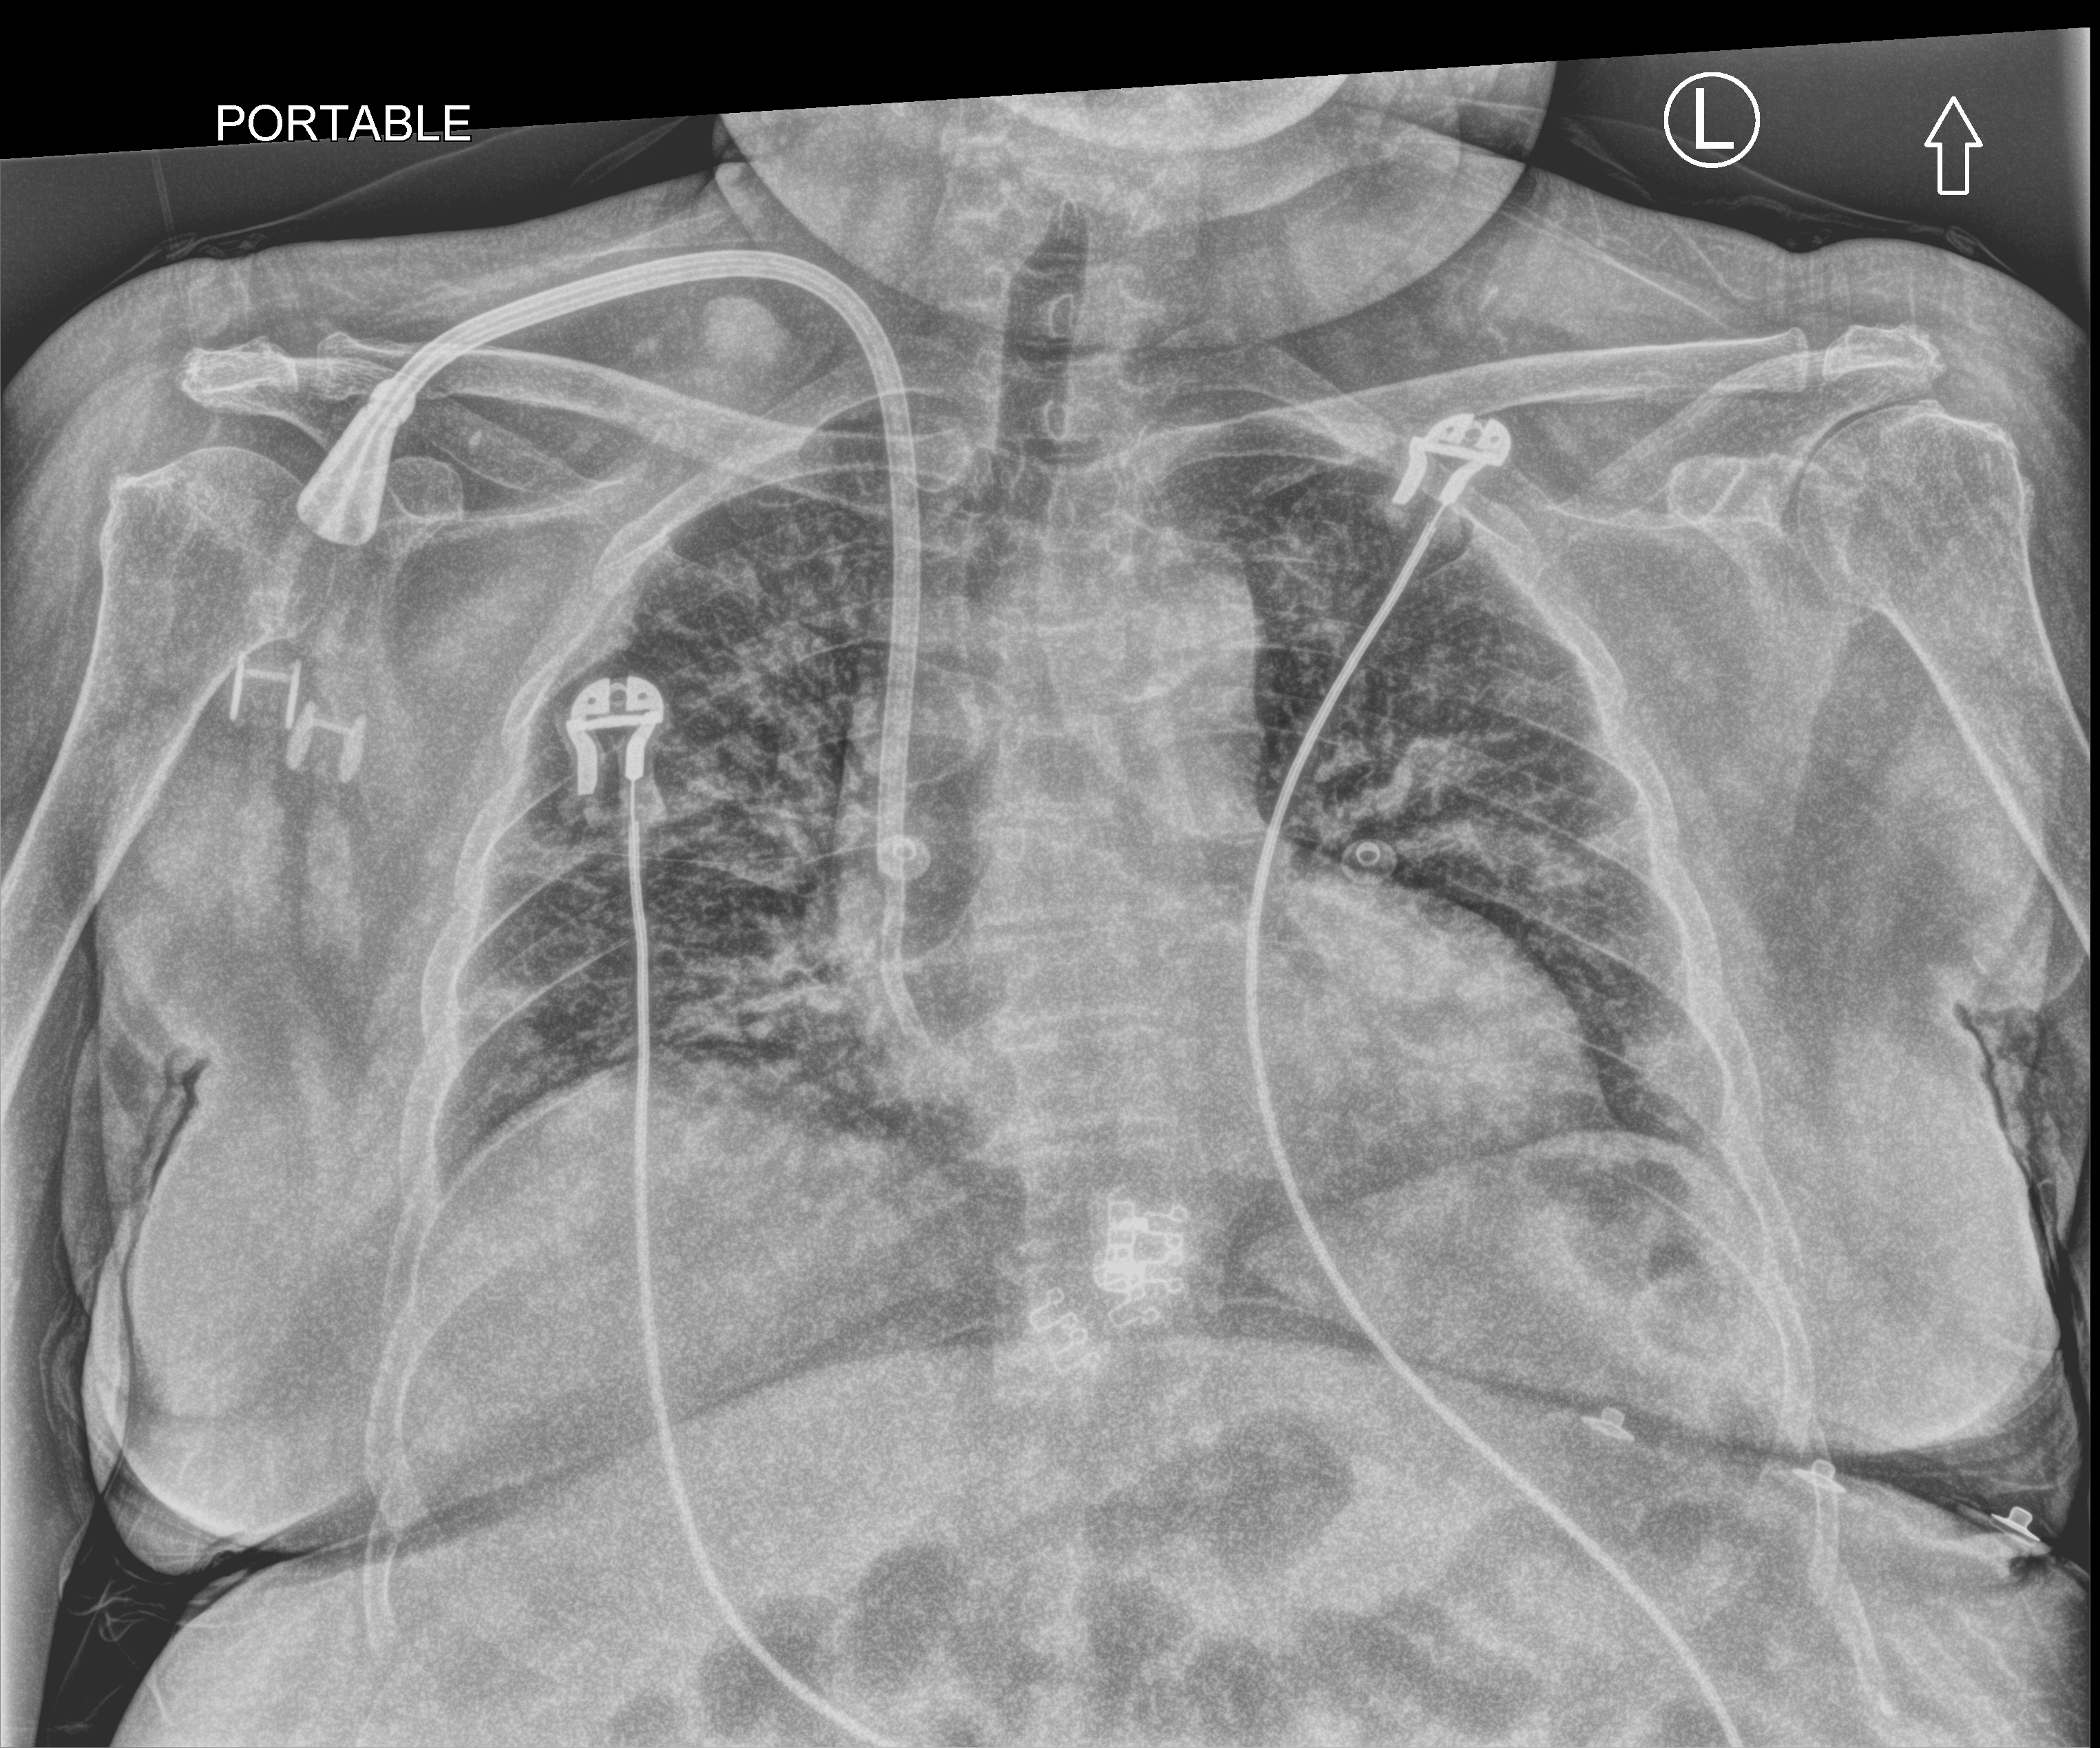
Portable chest radiograph. Female patient hospitalised with COVID-19, age 60–74 years.
Admission-level facts for this patient (not findings on this image; timing relative to this image not recorded):
- admitted to intensive care during this hospital stay: no